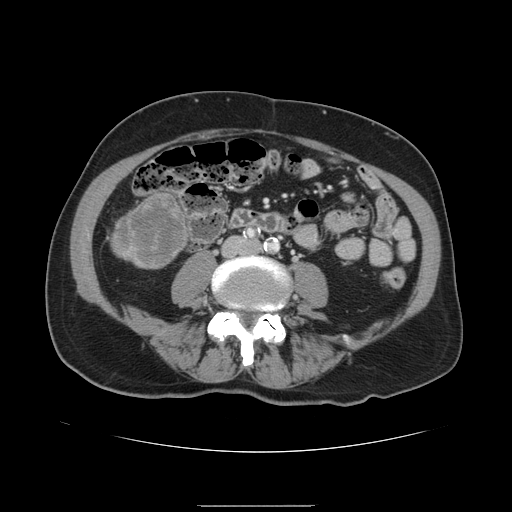
Contrast-enhanced abdominal CT, one axial slice; slice 16 of 168 in the series (ordered by position); intravenous contrast given; soft-tissue window (W 400 / L 40 HU); 2.5 mm slice thickness; 512 × 512 image matrix, field of view 386 × 386 mm. Male patient, age 74 years. From the clinical record (not read from this slice): diagnosis: colorectal cancer liver metastases, imaged before liver resection; multiple liver metastases: no.
Structures marked on this image (expert manual segmentation):
- liver: bounding box (x1, y1, x2, y2) in pixels: (112, 190, 190, 269)
- liver metastasis: (116, 194, 186, 267)